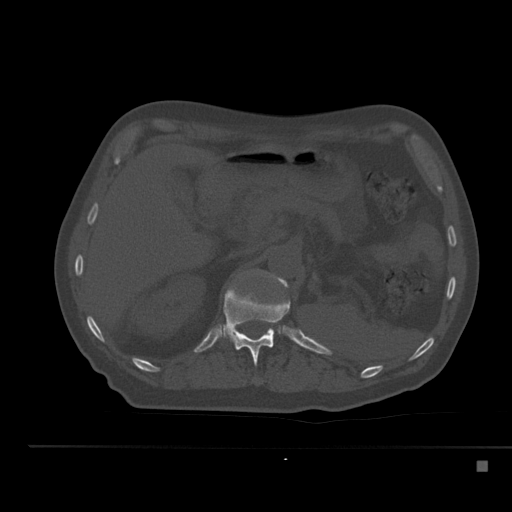
CT including the spine, one axial slice. 120 kVp. Bone window (W 1800 / L 400 HU). 1.5 mm slice thickness. 512 × 512 image matrix, field of view 408 × 408 mm. Male patient, age 70 years. From the clinical record (not read from this slice): primary cancer: renal.
Annotated regions visible in this slice (semi-automatic segmentation, software-assisted and operator-edited):
- L1 vertebra: box from (x=260, y=271) to (x=288, y=332) px
- T12 vertebra: (x=223, y=287)–(x=290, y=366)